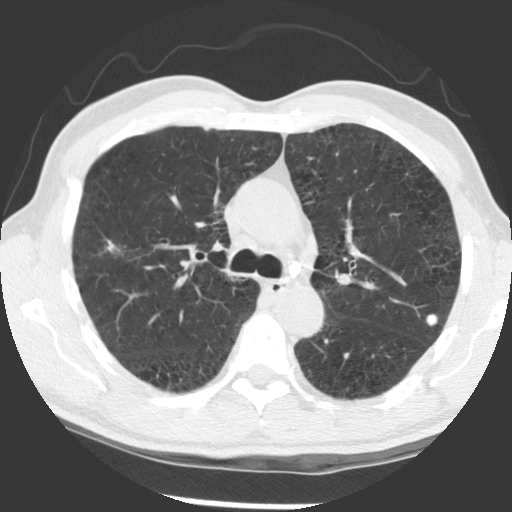
Low-dose screening chest CT, axial slice; baseline screening round; lung window (W 1500 / L -600 HU); 2.5 mm slice thickness; 140 kVp; slice 93 of 140 in the series; 512 × 512 image matrix, field of view 321 × 321 mm. Male, age 56 years at enrolment. Current smoker at enrolment.
Lesion marked by an expert reader, bounding box (x1, y1, x2, y2) in pixels: (62, 222, 130, 274). Reader record for this screening exam (exam-level; its link to the box is not recorded): non-calcified nodule or mass ≥4 mm, right upper lobe, 12 × 7 mm, spiculated (stellate) margins, soft tissue attenuation. Official screen result: positive, change unspecified: nodule(s) >= 4 mm or enlarging nodule(s), mass(es), or other non-specific abnormalities suspicious for lung cancer. Later outcome: lung cancer diagnosed 676 days after this screen (after the second annual screen) — squamous cell carcinoma, NOS, right upper lobe, right middle lobe, moderately differentiated (G2), stage IB (AJCC 6th edition), 70 mm at pathology.